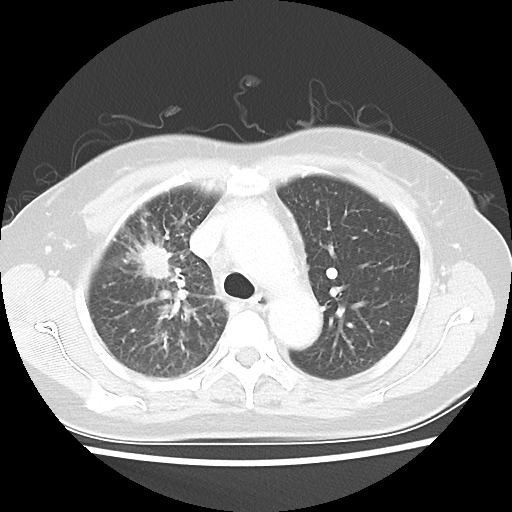
Chest CT, one axial slice; position 32 of 48 along the scan axis; reconstruction kernel LUNG; lung window (W 1500 / L -600 HU); 512 × 512 image matrix. Patient: female, 55 years. From the clinical record (not read from this slice): clinical TNM (as recorded): T1b N3 M1a.
Structures marked on this image (rectangle marked by the reading radiologist):
- lung tumour (recorded histology: adenocarcinoma): box from (x=131, y=243) to (x=172, y=279) px